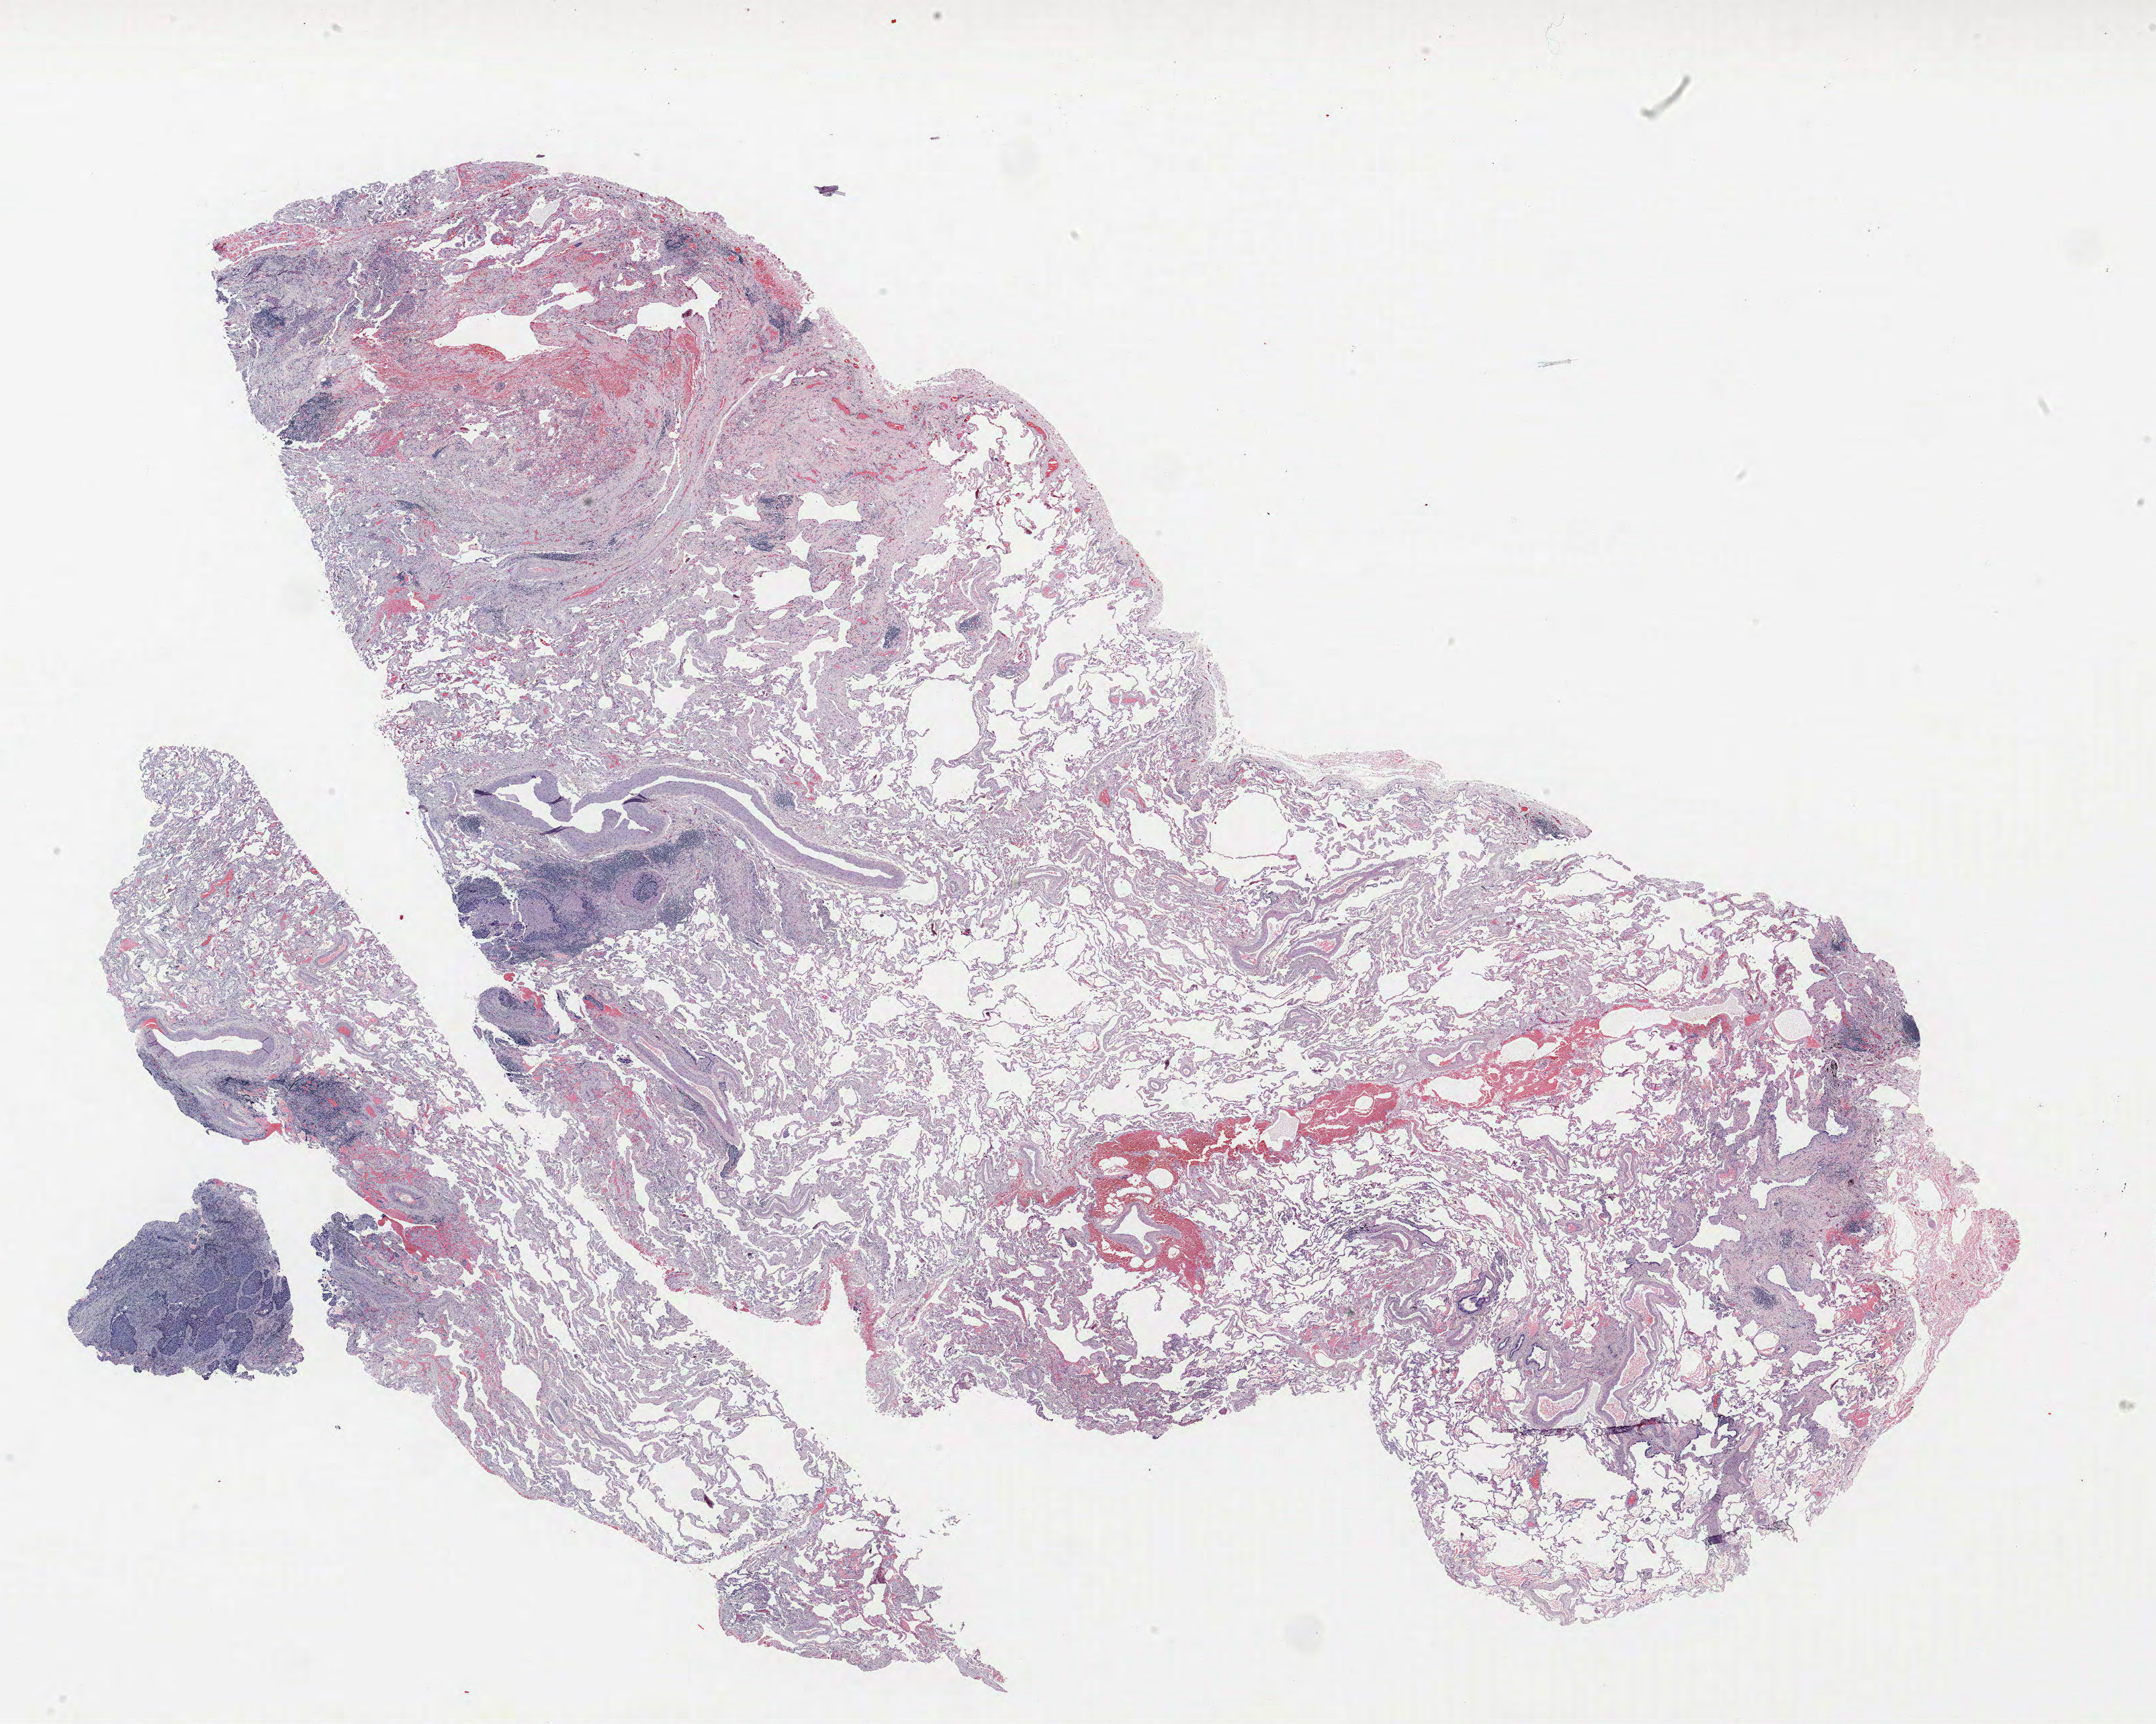
Whole-slide histology image, Hematoxylin and eosin (H&E) stained — low-resolution overview of the scanned area, about 25.7 x 20.5 mm. Formalin-fixed paraffin-embedded (FFPE) section. Lung tissue. Male, age 68 at enrolment. Former smoker at enrolment. Grade: moderately differentiated (G2).
- primary tumour location (clinical record): left upper lobe
- stage (AJCC 6th edition): IA
- tumour size (pathology): 17 mm
- participant's lung-cancer diagnosis: Squamous cell carcinoma, NOS (ICD-O-3 8070/3)